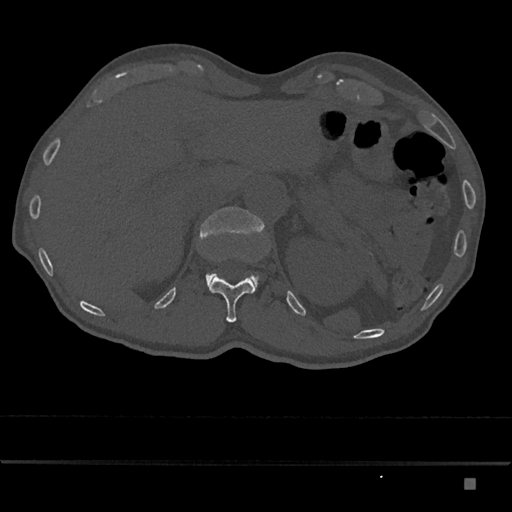
CT including the spine, one axial slice. Slice 590 of 797 in the series (ordered by position). Reconstruction kernel Br40s/3. 120 kVp. Bone window (W 1800 / L 400 HU). 0.5 mm slice thickness. 512 × 512 image matrix. Male patient, age 72 years. Case-level facts recorded for this patient, not image findings: primary cancer: prostate.
Structures marked on this image (semi-automatic segmentation, software-assisted and operator-edited):
- L1 vertebra: bounding box <200,207,265,290> (left, top, right, bottom; pixels)
- T12 vertebra: <209,276,255,323>